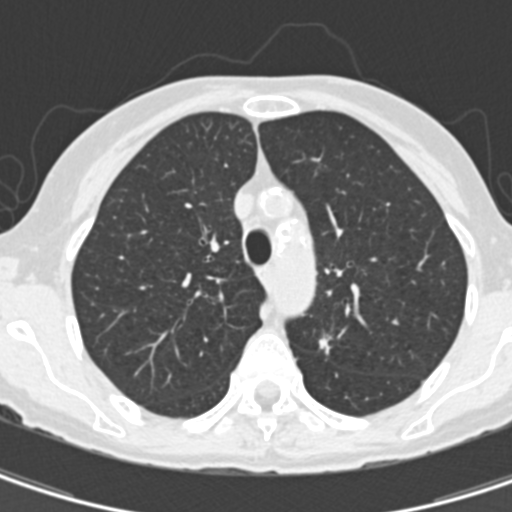
Low-dose screening chest CT, axial slice, baseline annual screen, lung window (W 1500 / L -600 HU), 2 mm slice thickness, standard (soft-tissue) reconstruction kernel (B30f). Female, age 67 years at enrolment. Current smoker at enrolment.
• Expert-annotated lung lesion, box from (x=308, y=321) to (x=349, y=373) px.
• The exam's reader record, not a measurement of the box and not confirmed to be the same lesion: non-calcified nodule or mass ≥4 mm, left upper lobe, 11 × 8 mm, spiculated (stellate) margins, soft tissue attenuation.
• Lung cancer was diagnosed 73 days after this screen: adenocarcinoma, NOS, left upper lobe, poorly differentiated (G3), stage IA (AJCC 6th edition), 13 mm at pathology.